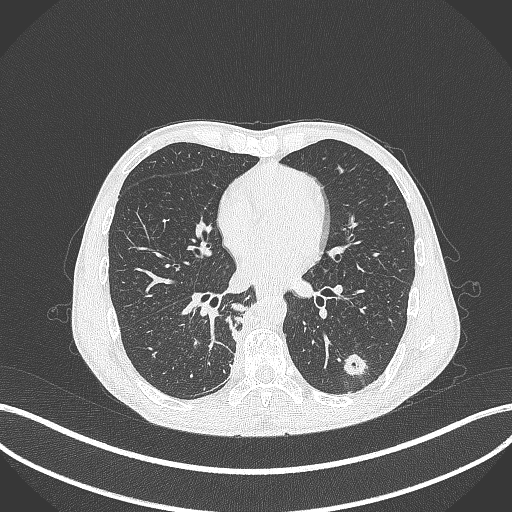
Chest CT, one axial slice. Position 169 of 371 along the scan axis. Reconstruction kernel B70f. 120 kVp. Lung window (W 1500 / L -600 HU). 512 × 512 image matrix. Patient: male, 58 years. From the clinical record (not read from this slice): clinical TNM (as recorded): T3 N1 M1.
Outlined on this slice (rectangle marked by the reading radiologist):
- lung tumour (recorded histology: squamous cell carcinoma): box from (x=340, y=350) to (x=370, y=378) px